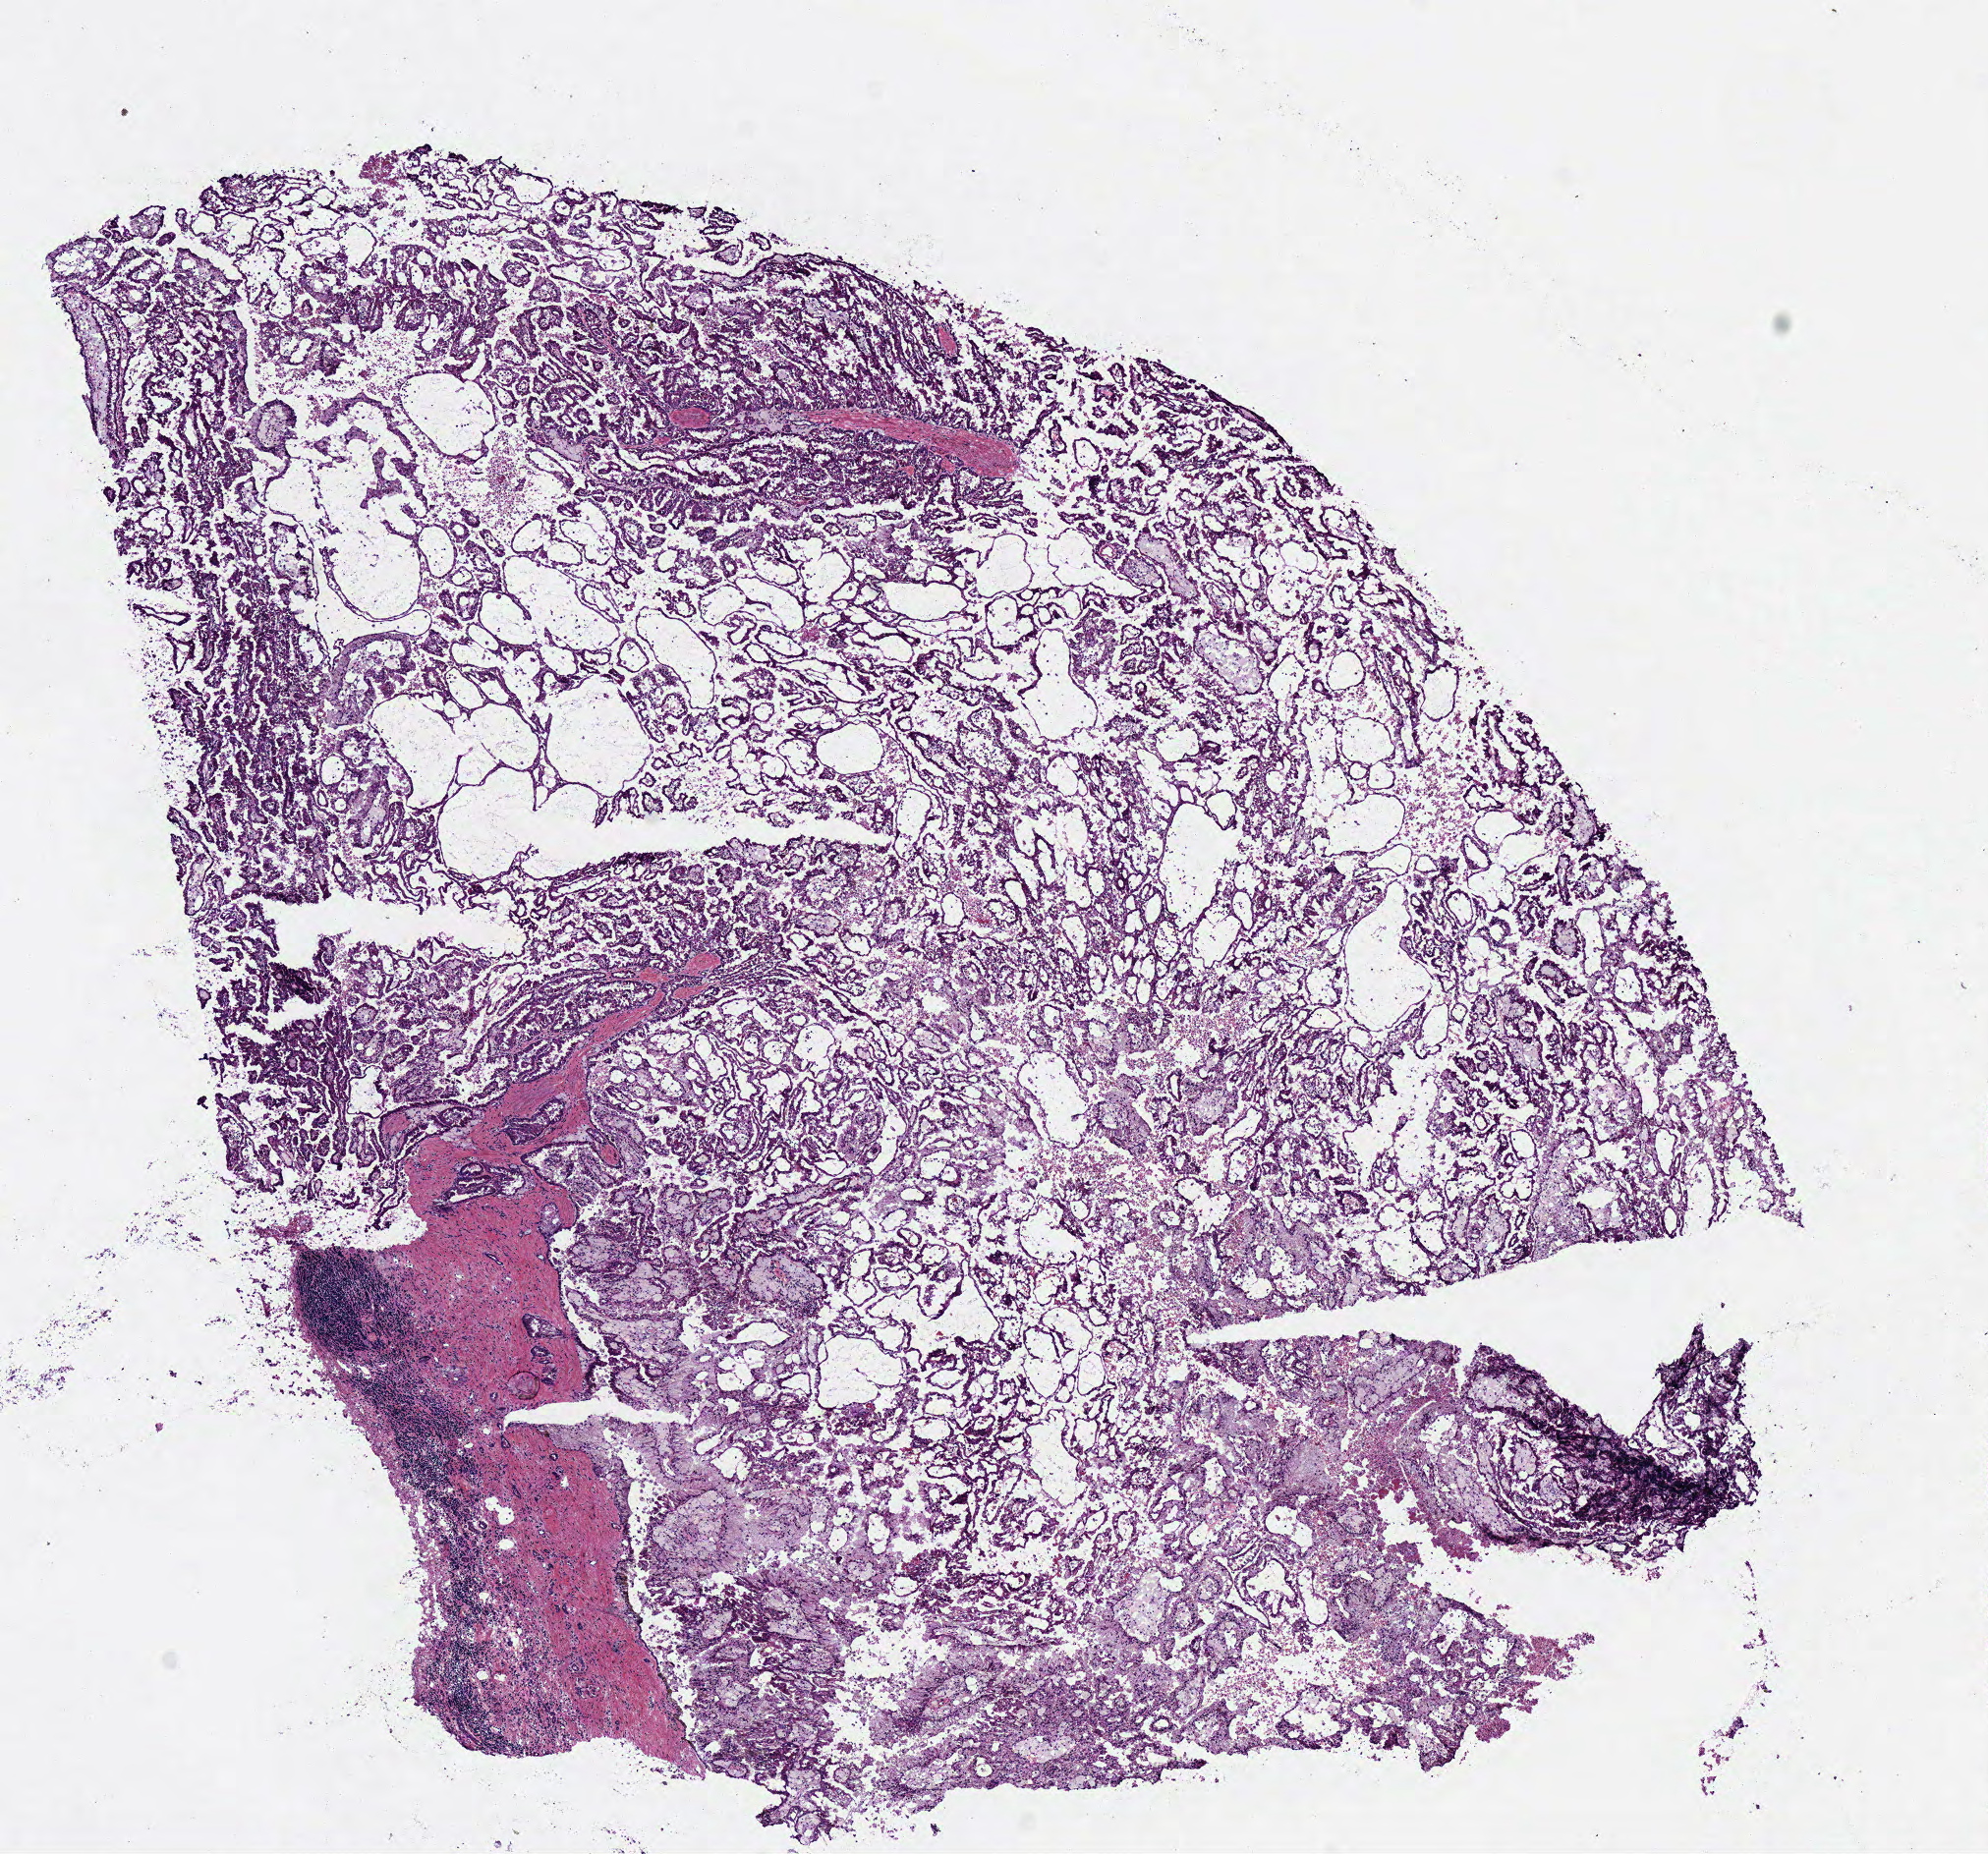
Digitized H&E tissue section (whole slide) — shown as a low-resolution overview of the whole scanned area (about 8.0 x 7.4 mm), frozen section from the bottom of the tissue portion, kidney, primary tumour sample. Patient: male, age at initial diagnosis 69 years. Slide review estimates, as recorded: tumour cells 72%, tumour nuclei 75%, normal cells 0%, stromal cells 20%, necrosis 3%. Inflammatory infiltration, as recorded: lymphocyte infiltration 10%, monocyte infiltration 10%, neutrophil infiltration 0%.
- diagnosis: Papillary adenocarcinoma, NOS
- AJCC pathologic stage: I